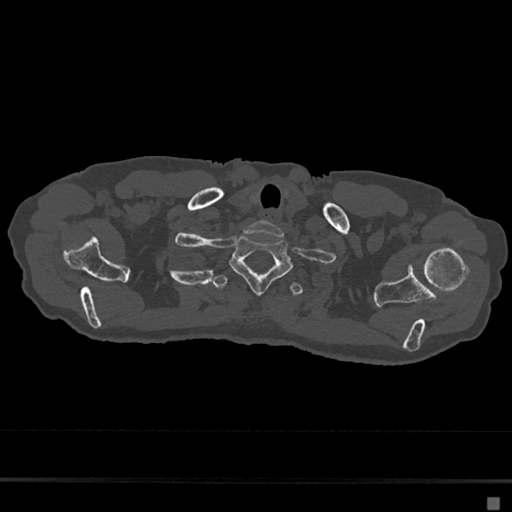
CT including the spine, one axial slice; position 605 of 797 along the scan axis; 120 kVp; bone window (W 1800 / L 400 HU); 512 × 512 image matrix, field of view 360 × 360 mm. Female patient, age 68 years. Case-level facts recorded for this patient, not image findings: primary cancer: renal.
Structures marked on this image (semi-automatically segmented with operator editing):
- T1 vertebra: bounding box <230,235,292,295> (left, top, right, bottom; pixels)
- T2 vertebra: <213,275,303,296>